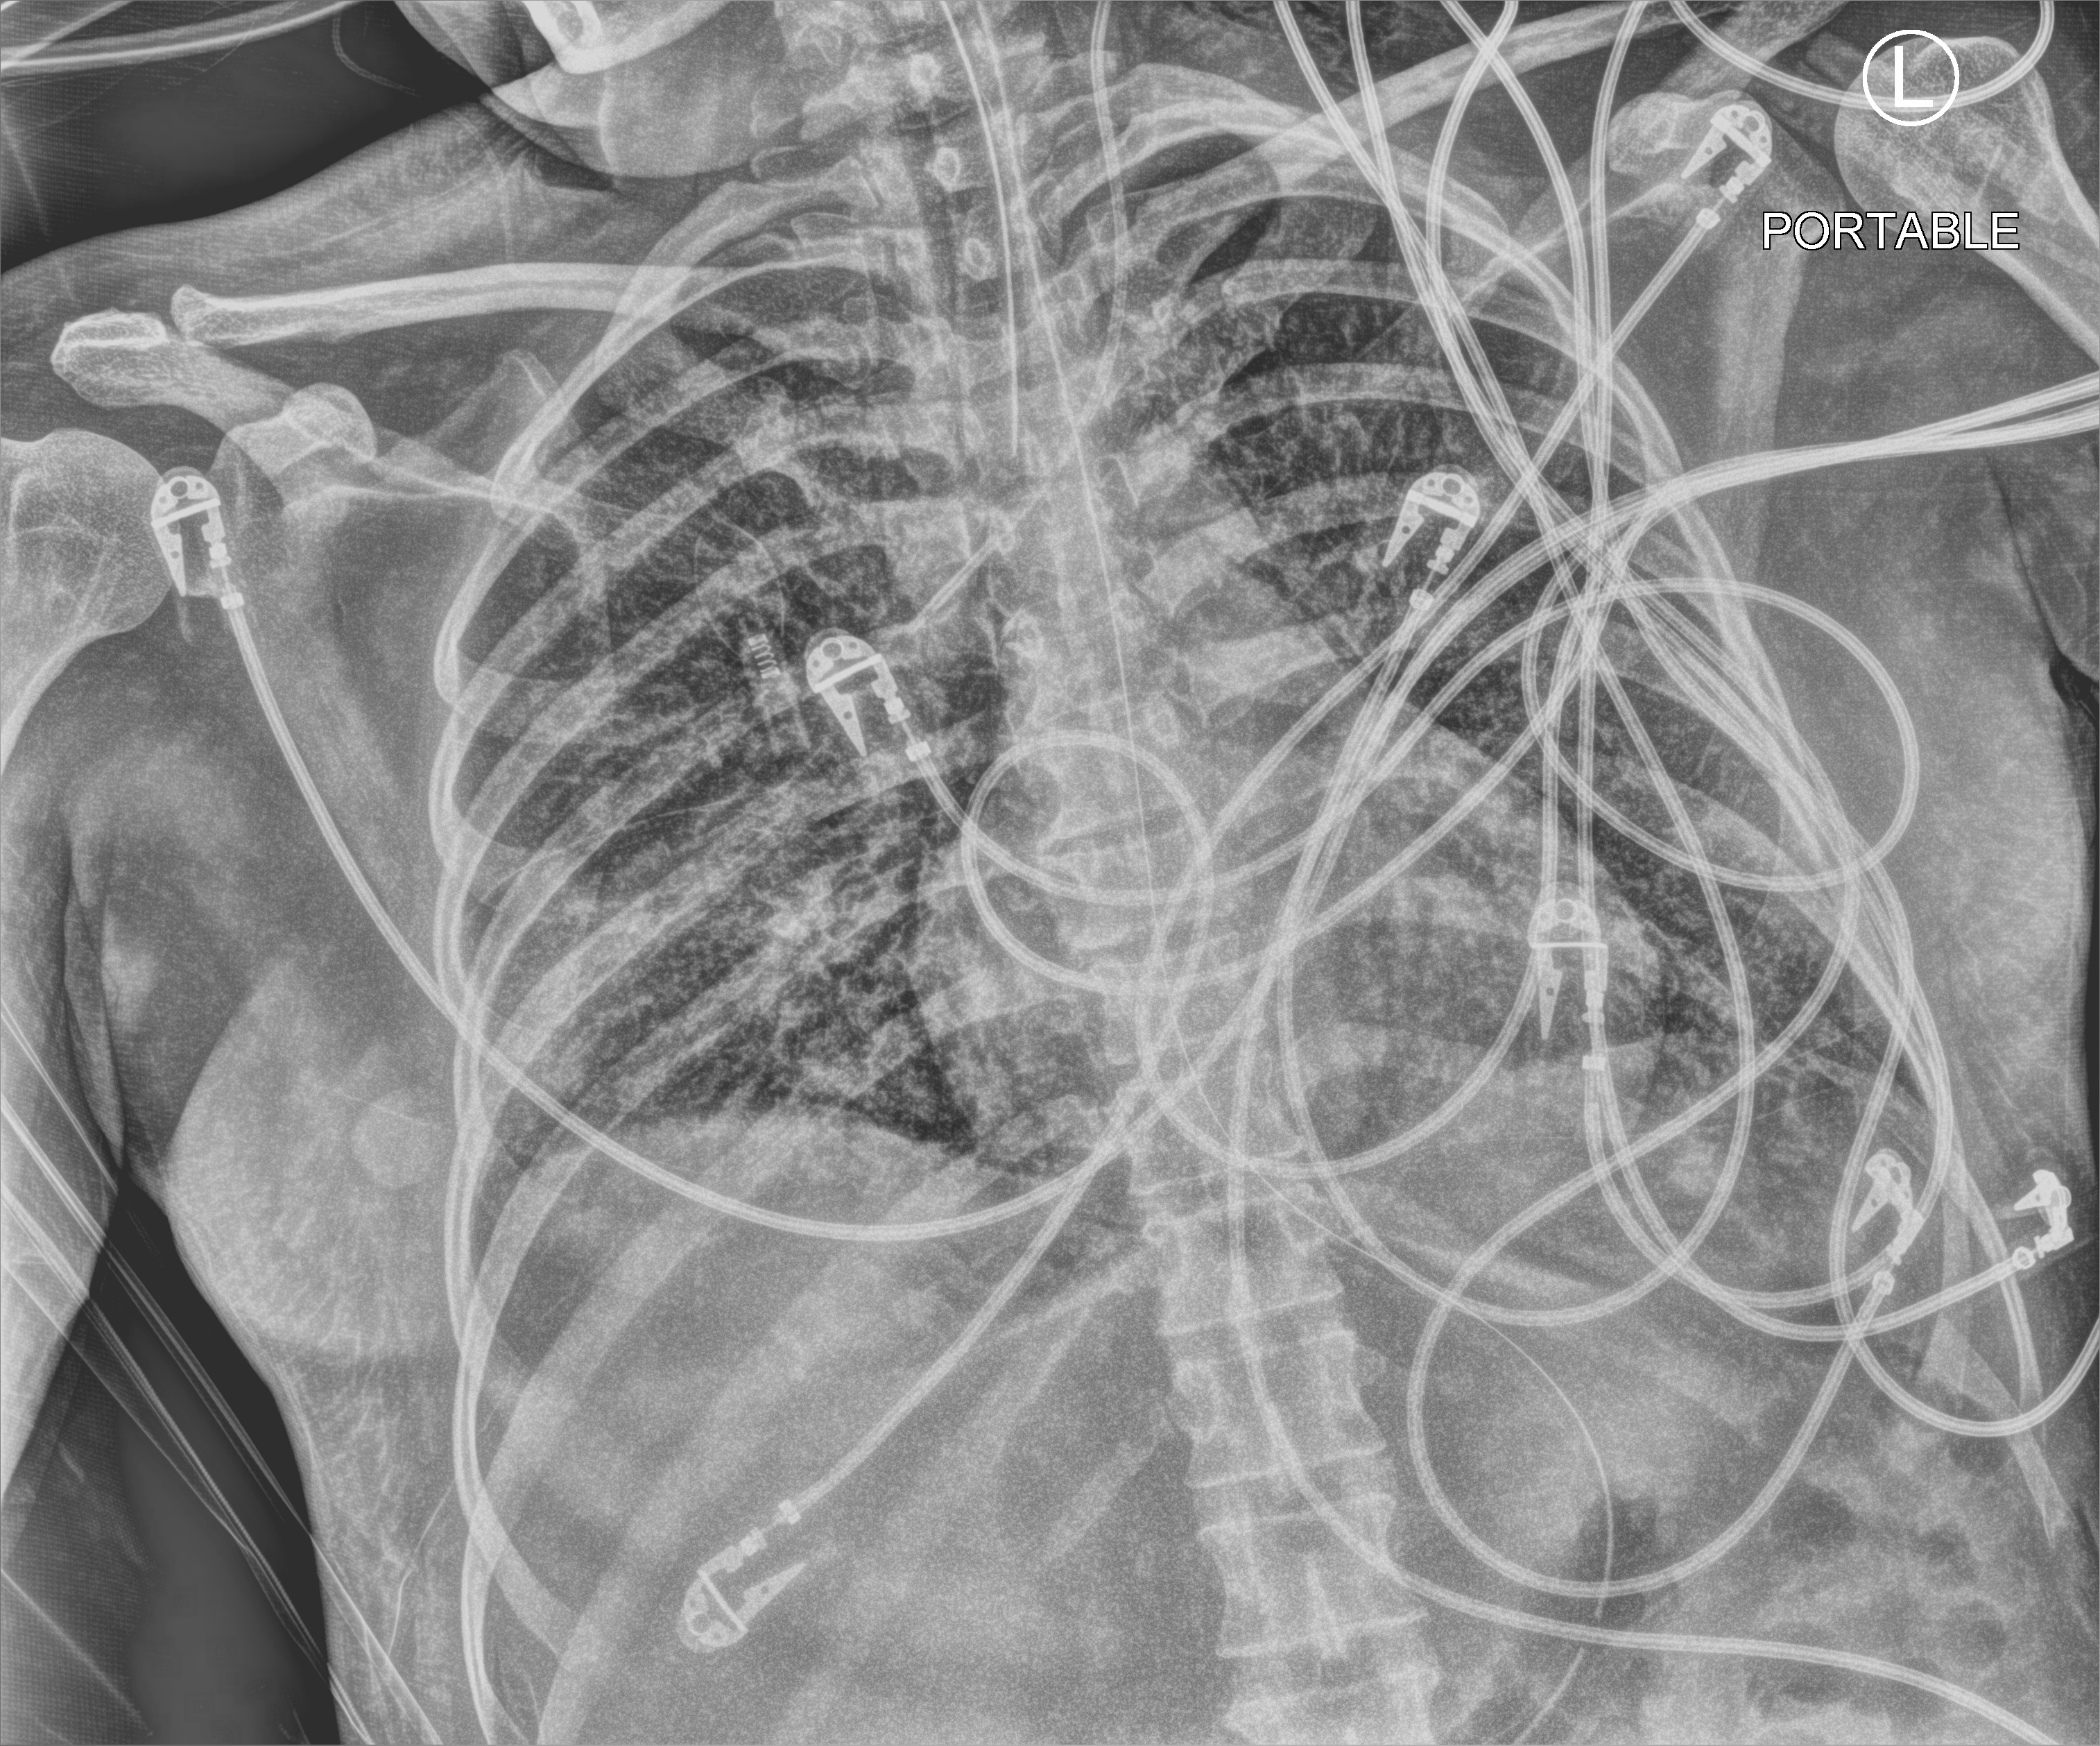
Bedside chest radiograph (computed radiography), anteroposterior (AP) projection. Patient hospitalised with COVID-19; female, aged 18–59 years.
From the hospital-stay record, not from the radiograph (when in the stay this image was taken is not recorded): mechanically ventilated during this hospital stay: yes.